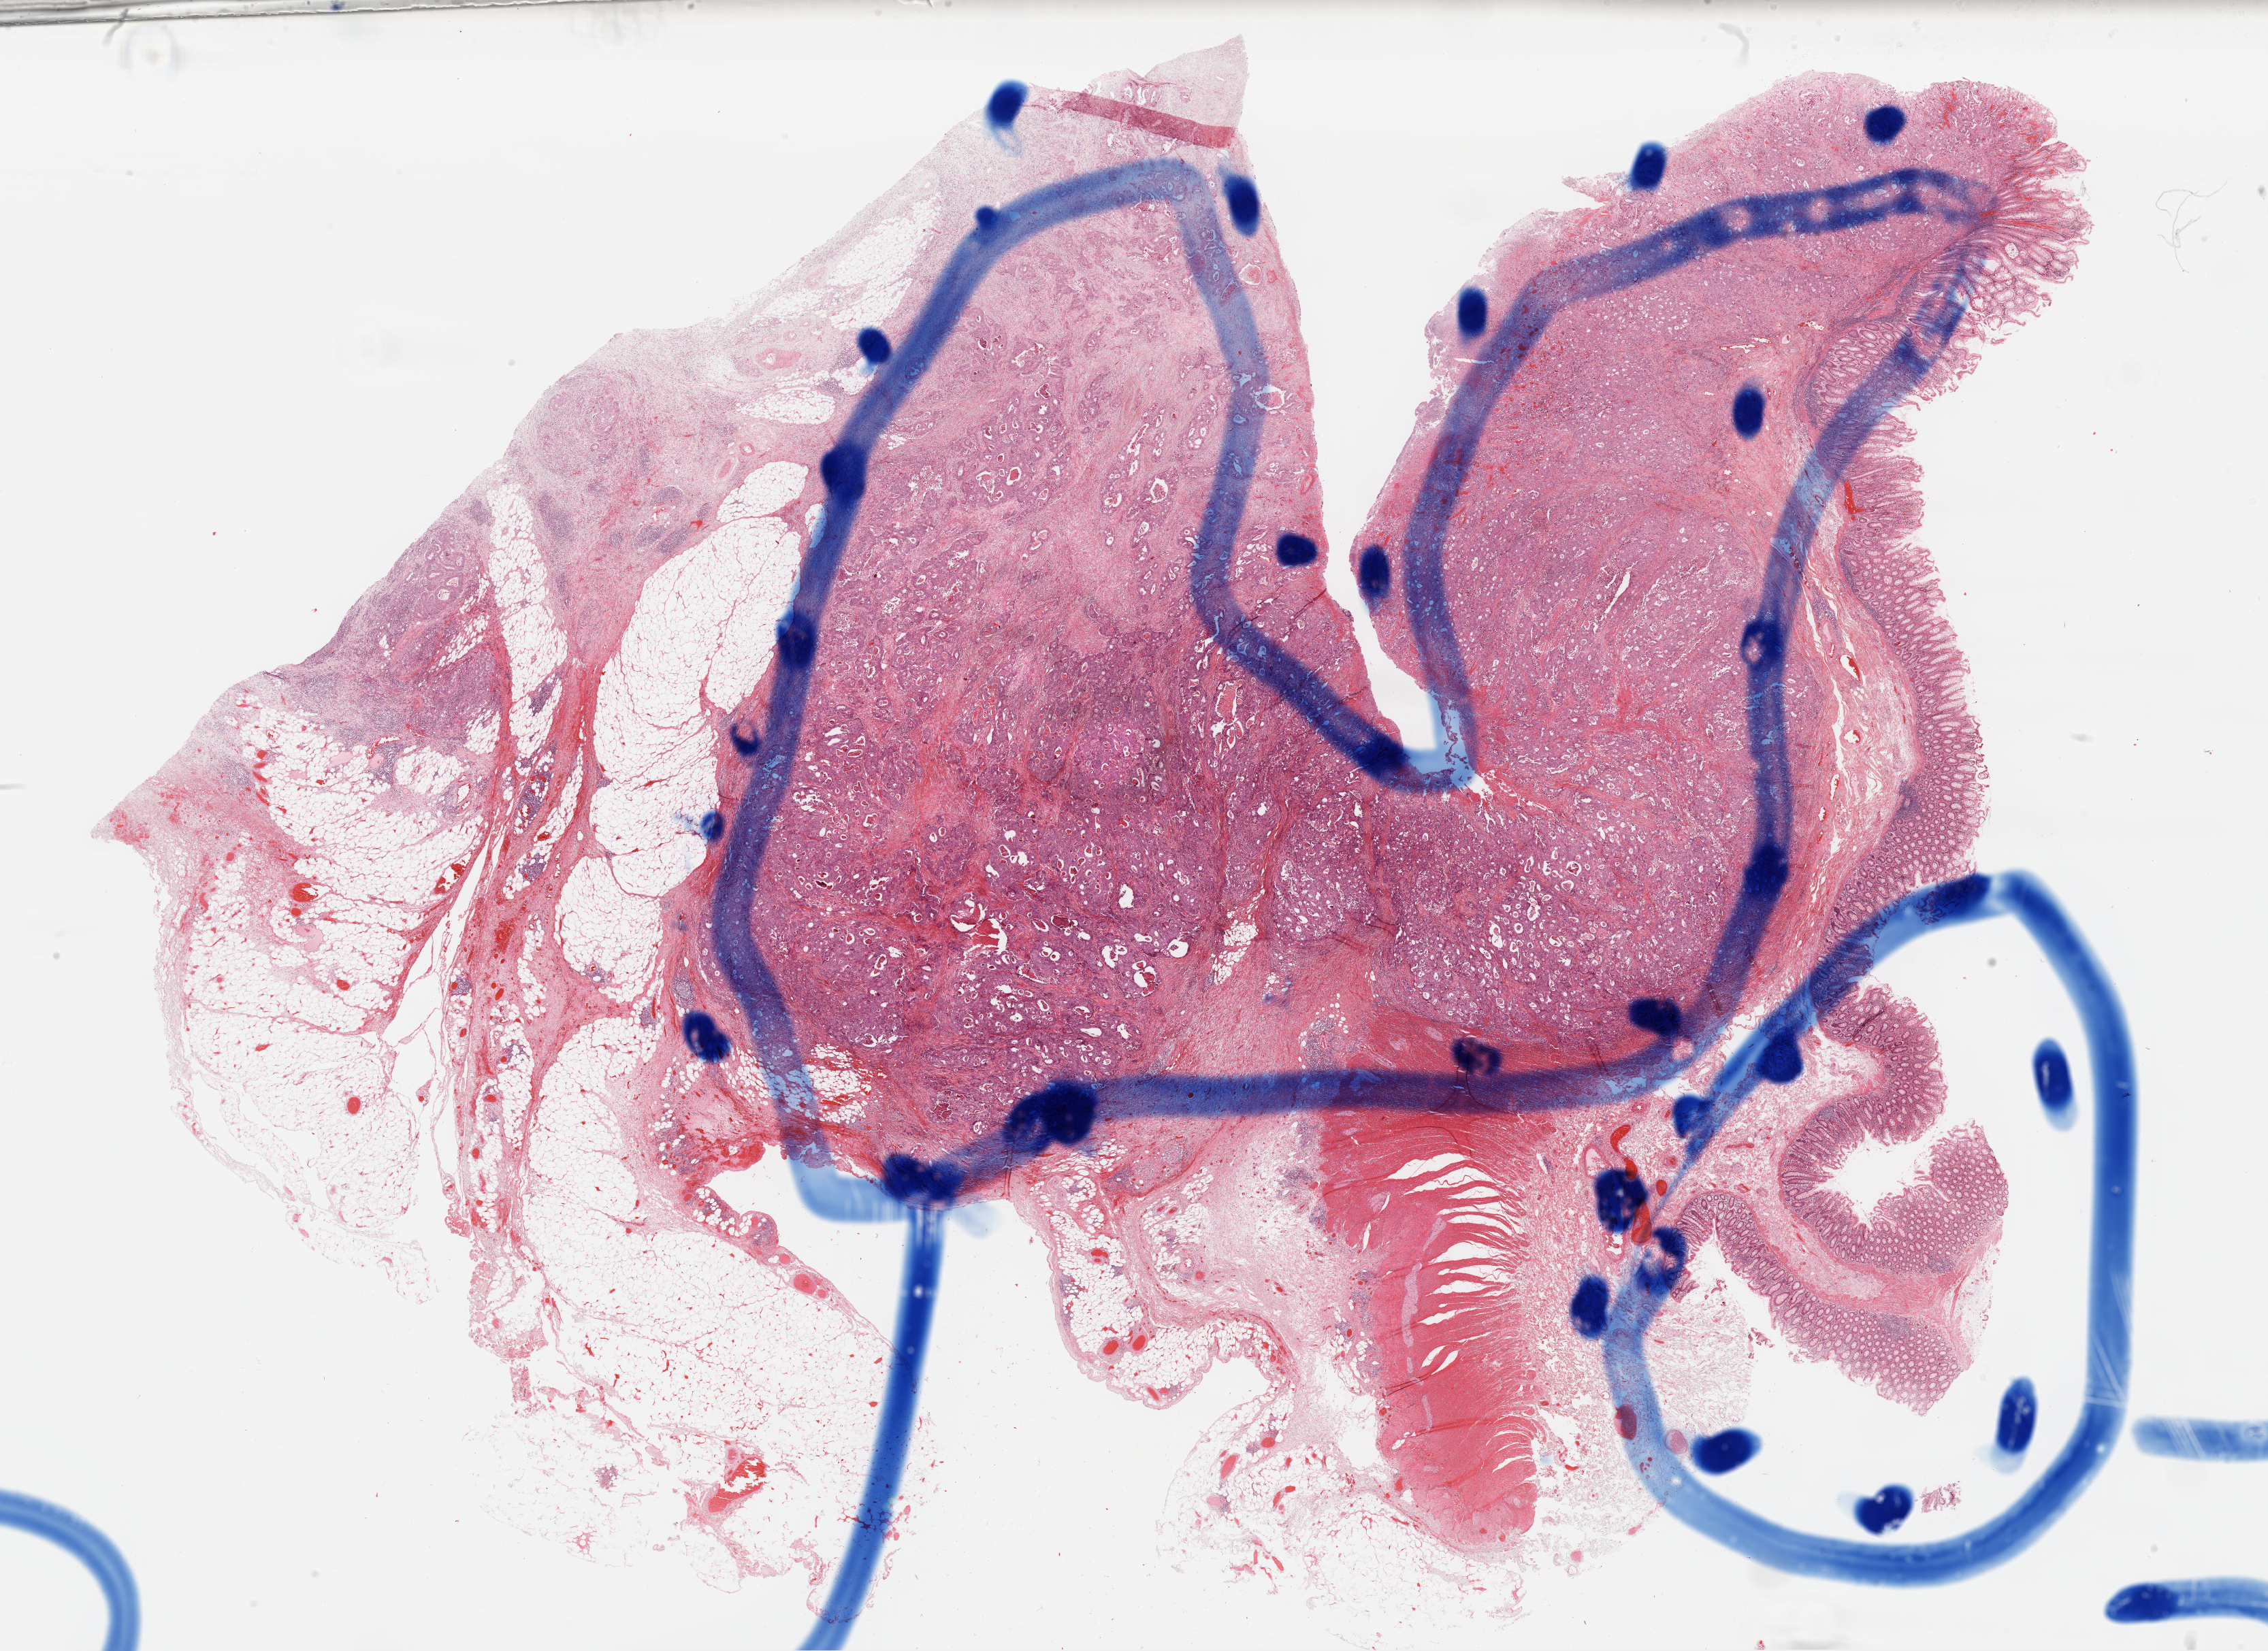
Digitized H&E tissue section (whole slide) — whole scanned area (about 26.3 x 19.2 mm, from a 40x scan) shown as a low-resolution overview, FFPE section, primary tumour sample from the colon. Male patient; age at initial diagnosis 78 years.
- lymph nodes positive (case pathology): 6 of 15 examined
- AJCC pathologic stage: IIIC (6th edition)
- pathologic diagnosis: Adenocarcinoma, NOS (cecum)